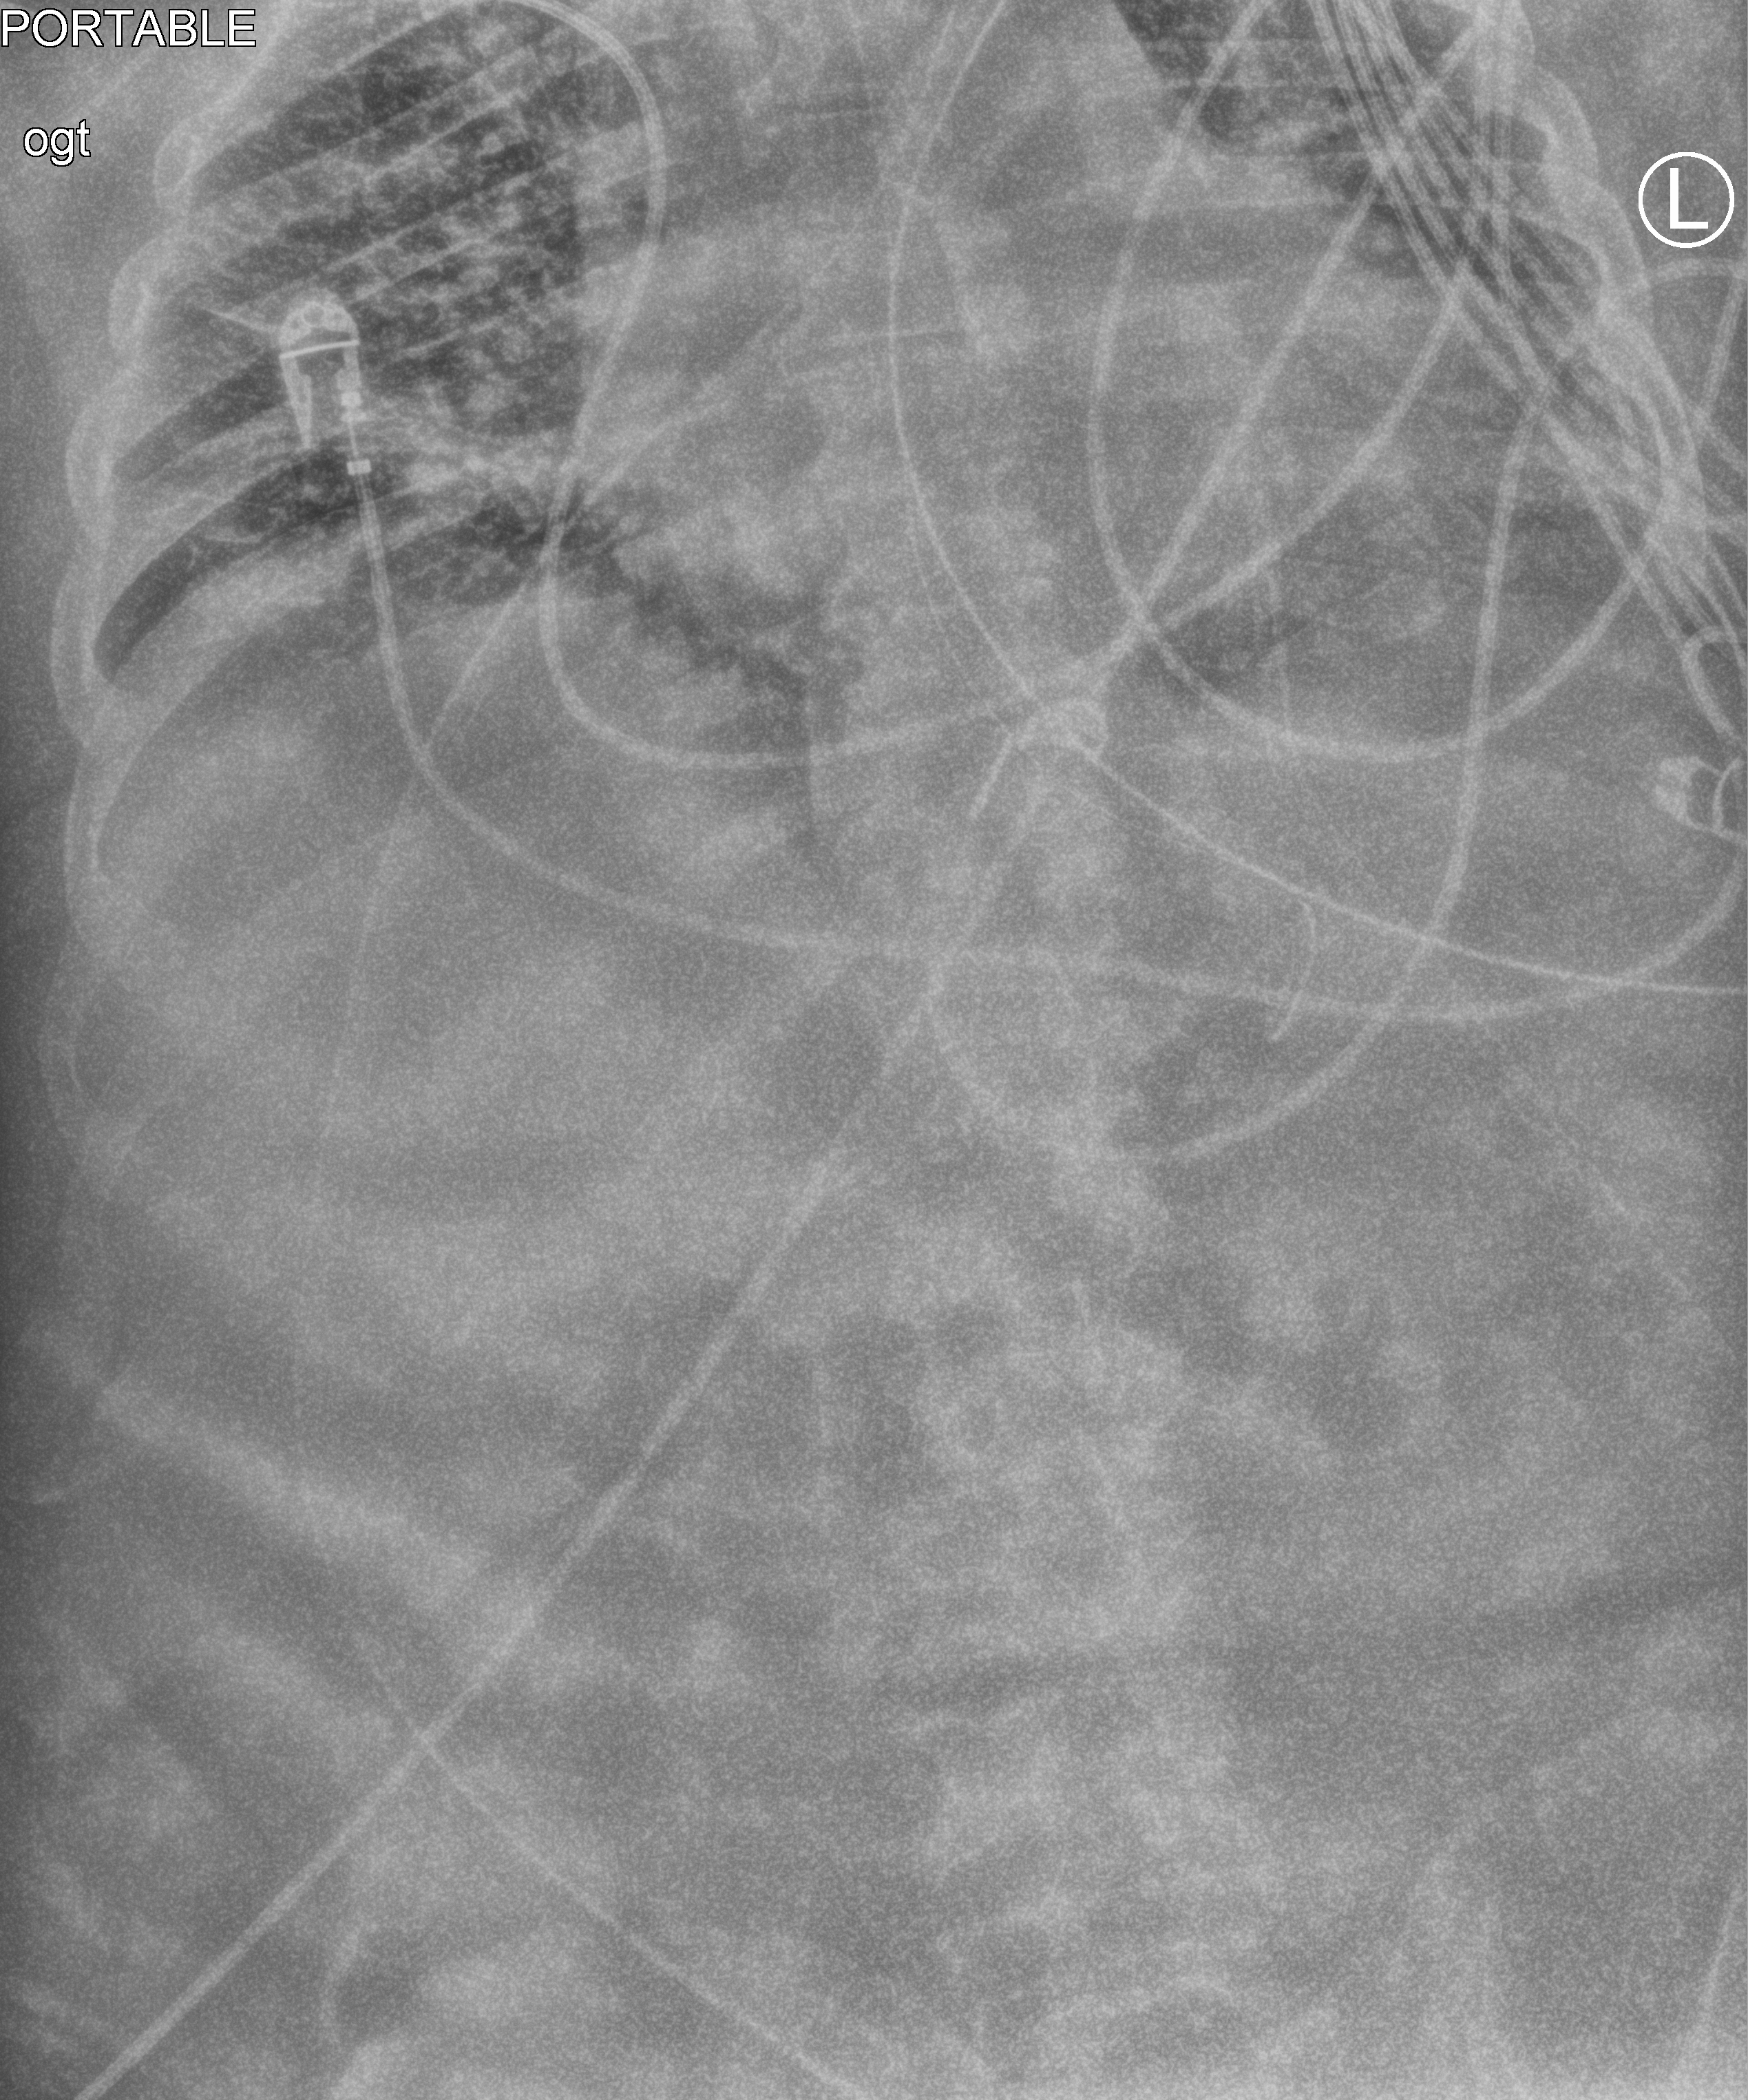
Bedside chest radiograph (computed radiography). Patient hospitalised with COVID-19; male, aged 18–59 years.
From the hospital-stay record, not from the radiograph (when in the stay this image was taken is not recorded): admitted to intensive care during this hospital stay: yes; mechanically ventilated during this hospital stay: yes.